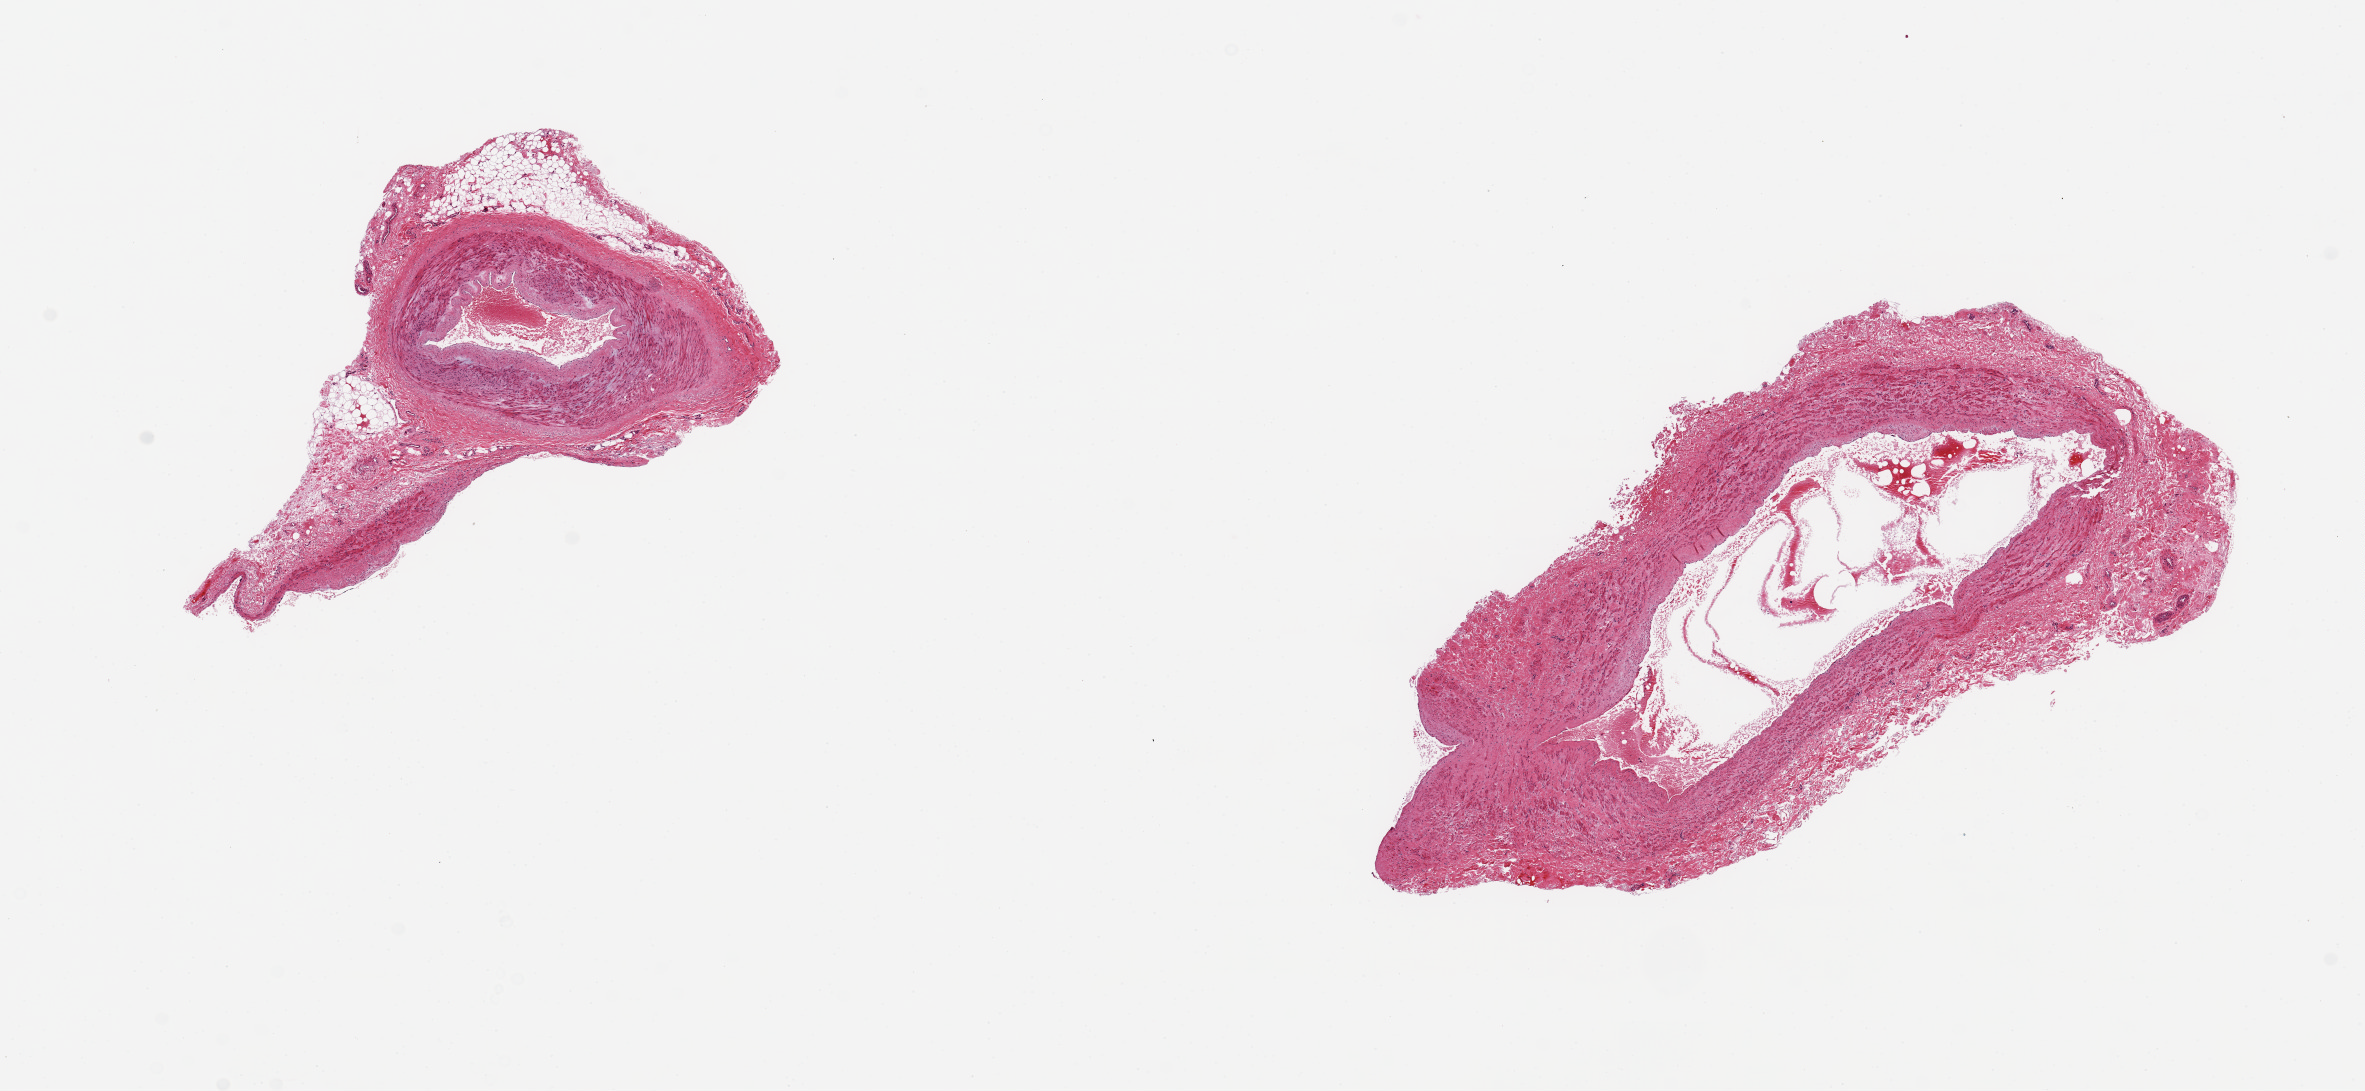
Haematoxylin and eosin whole-slide image — shown as a low-resolution overview of the whole scanned area (about 18.7 x 8.6 mm); PAXgene-fixed, paraffin-embedded tissue; sampled site (target tissue): tibial artery; donor tissue sample. Donor: male.
Pathologist's review note for this sample: 2 ~2.5mm pieces, with 0.5-1mm rim of fat/fibrous tissue.